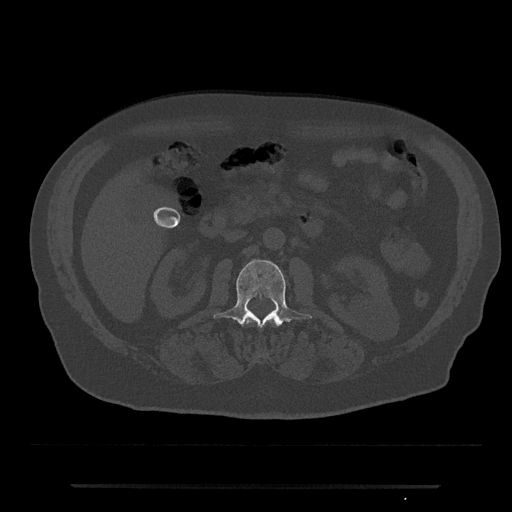
CT including the spine, one axial slice; reconstruction kernel Br40s/3; 120 kVp; bone window (W 1800 / L 400 HU); 512 × 512 image matrix. Male patient, age 80 years. From the clinical record (not read from this slice): primary cancer: prostate; vertebrae with lytic lesions (as recorded): L1, T11.
Structures marked on this image (semi-automatic segmentation, software-assisted and operator-edited):
- L1 vertebra: box from (x=243, y=320) to (x=278, y=326) px
- L2 vertebra: (x=214, y=259)–(x=312, y=329)